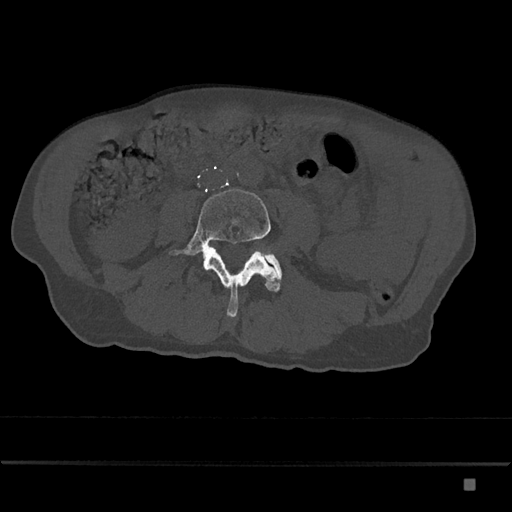
CT including the spine, one axial slice. Position 333 of 797 along the scan axis. Reconstruction kernel Br40s/3. 120 kVp. Bone window (W 1800 / L 400 HU). 0.5 mm slice thickness. 512 × 512 image matrix, field of view 390 × 390 mm. Patient: male, 72 years. From the clinical record (not read from this slice): primary cancer: prostate.
Annotated regions visible in this slice (semi-automatically segmented with operator editing):
- L4 vertebra: bounding box (x1, y1, x2, y2) in pixels: (169, 189, 282, 317)
- L5 vertebra: (267, 255, 282, 278)